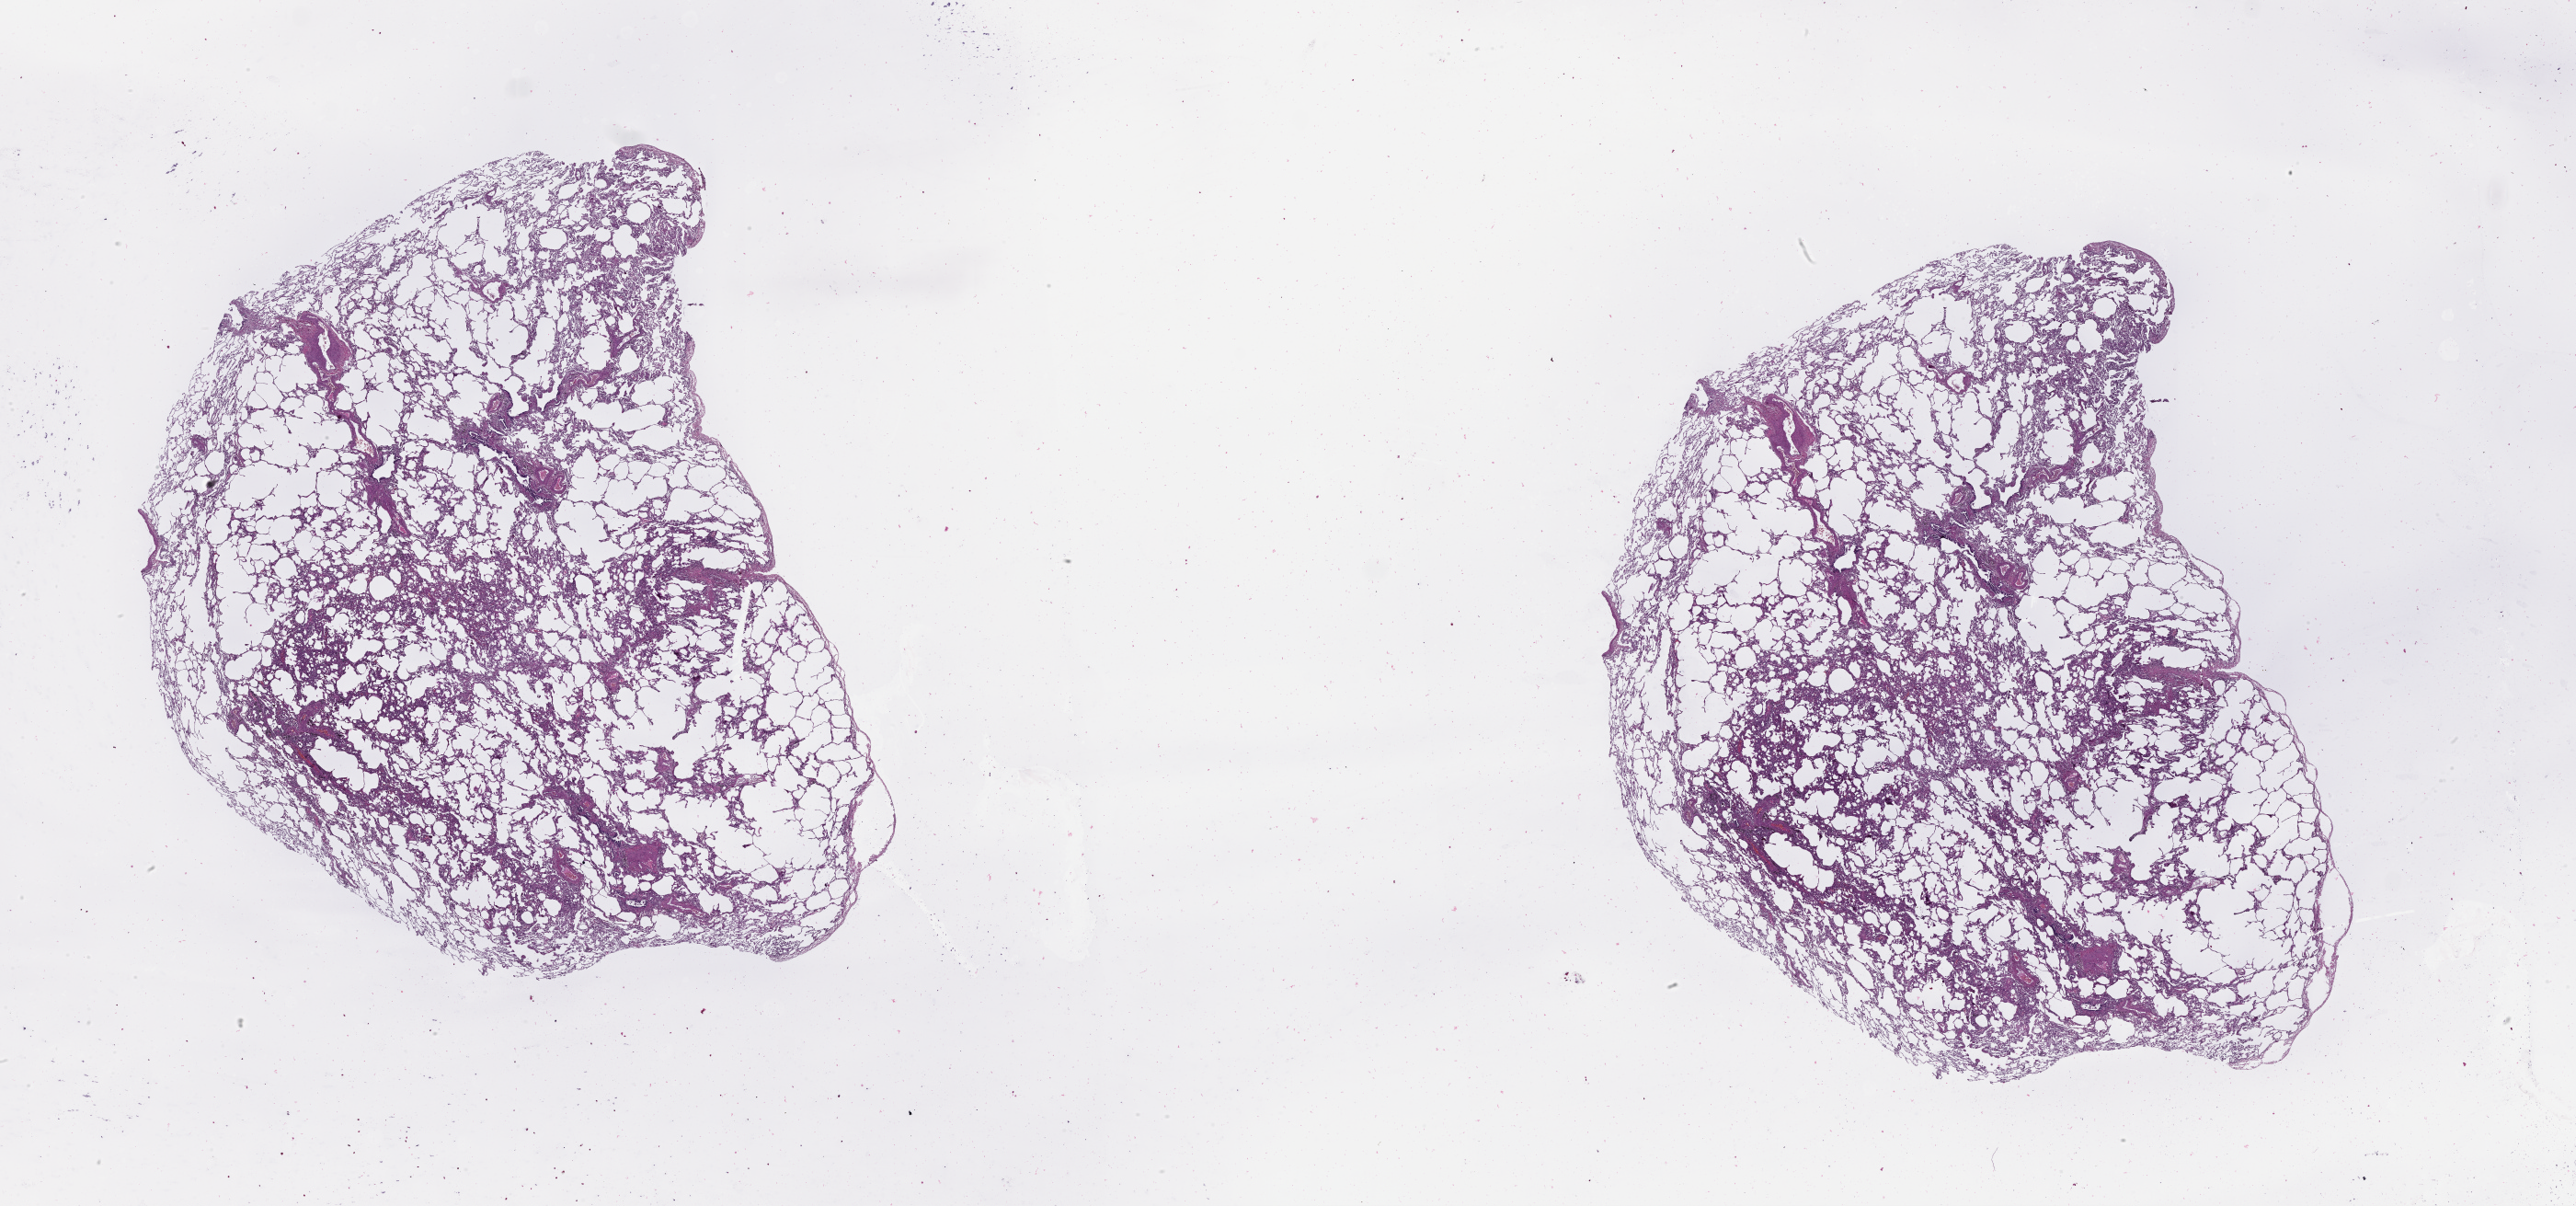
H&E-stained whole-slide image, shown as a low-resolution overview of the whole scanned area (about 45.1 x 21.1 mm, acquisition: 20x scan). Lung, tissue type not recorded.
Patient diagnosis (cohort enrolment): lung adenocarcinoma (lung).